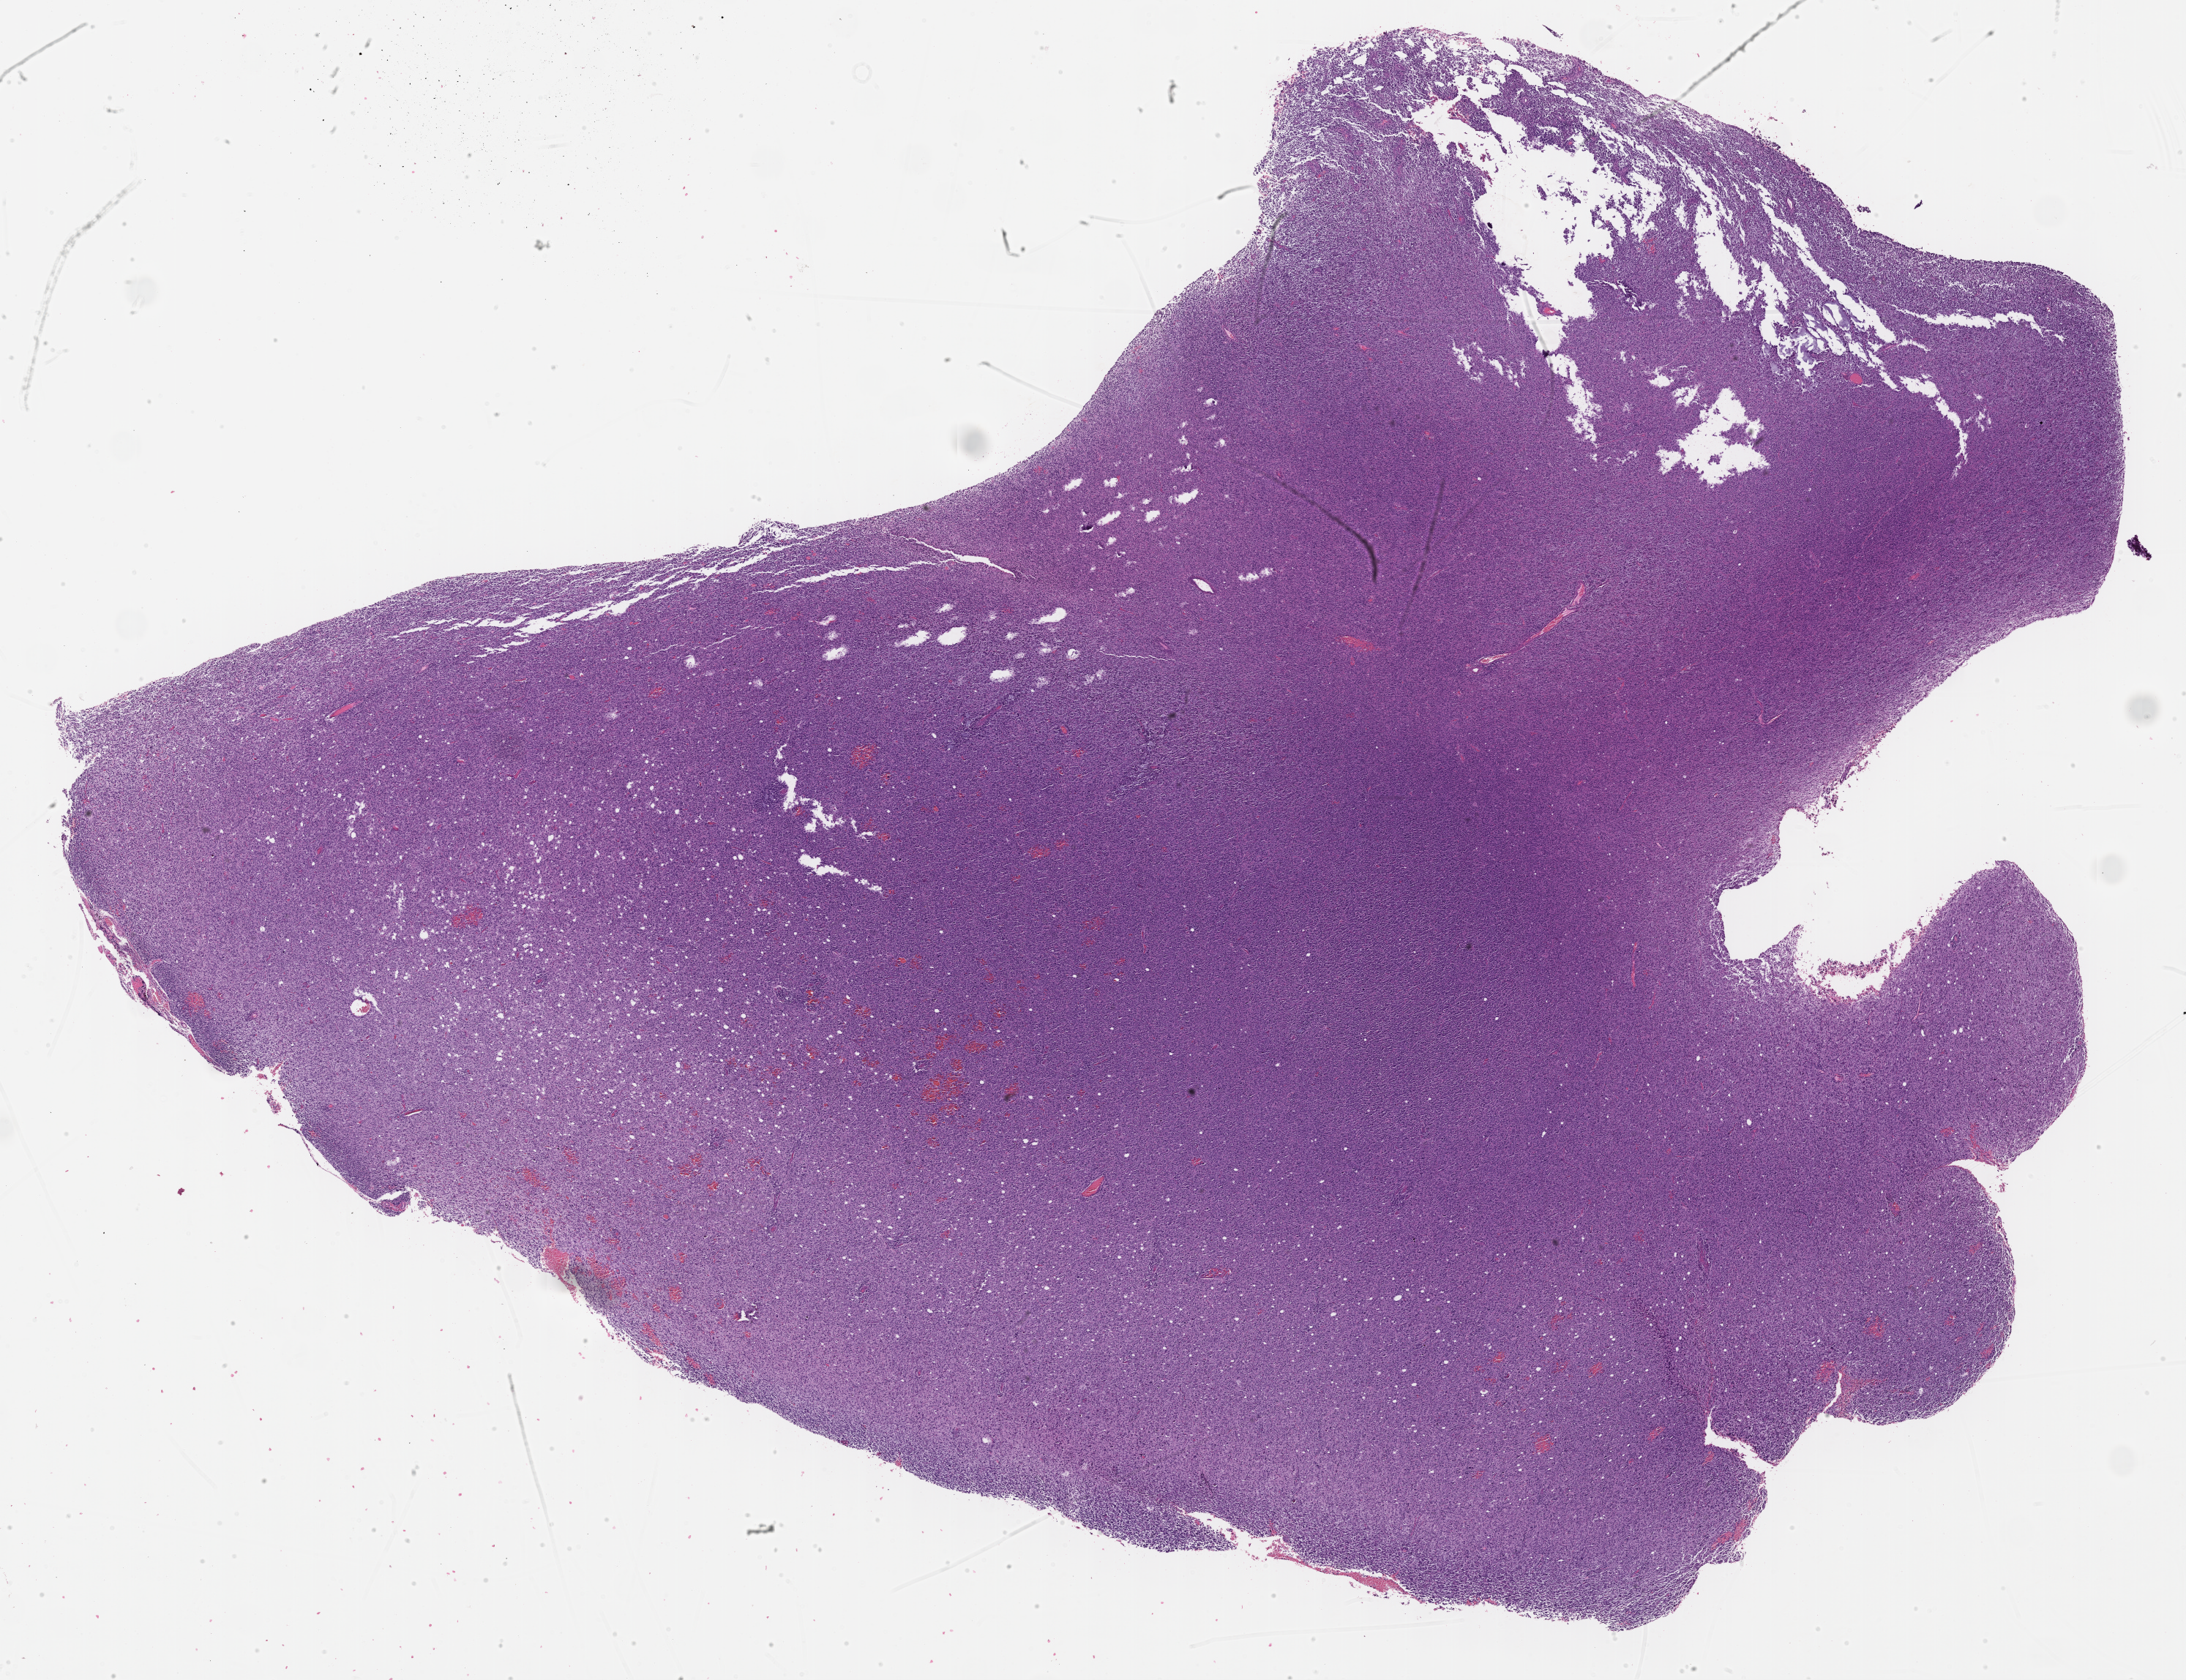
Digitized H&E-stained tissue section (whole slide) — whole scanned area (about 24.2 x 18.6 mm, from a 40x scan) shown as a low-resolution overview, FFPE section, primary tumour sample from the brain. Patient: male, age at initial diagnosis 46 years.
• histologic diagnosis: Glioblastoma